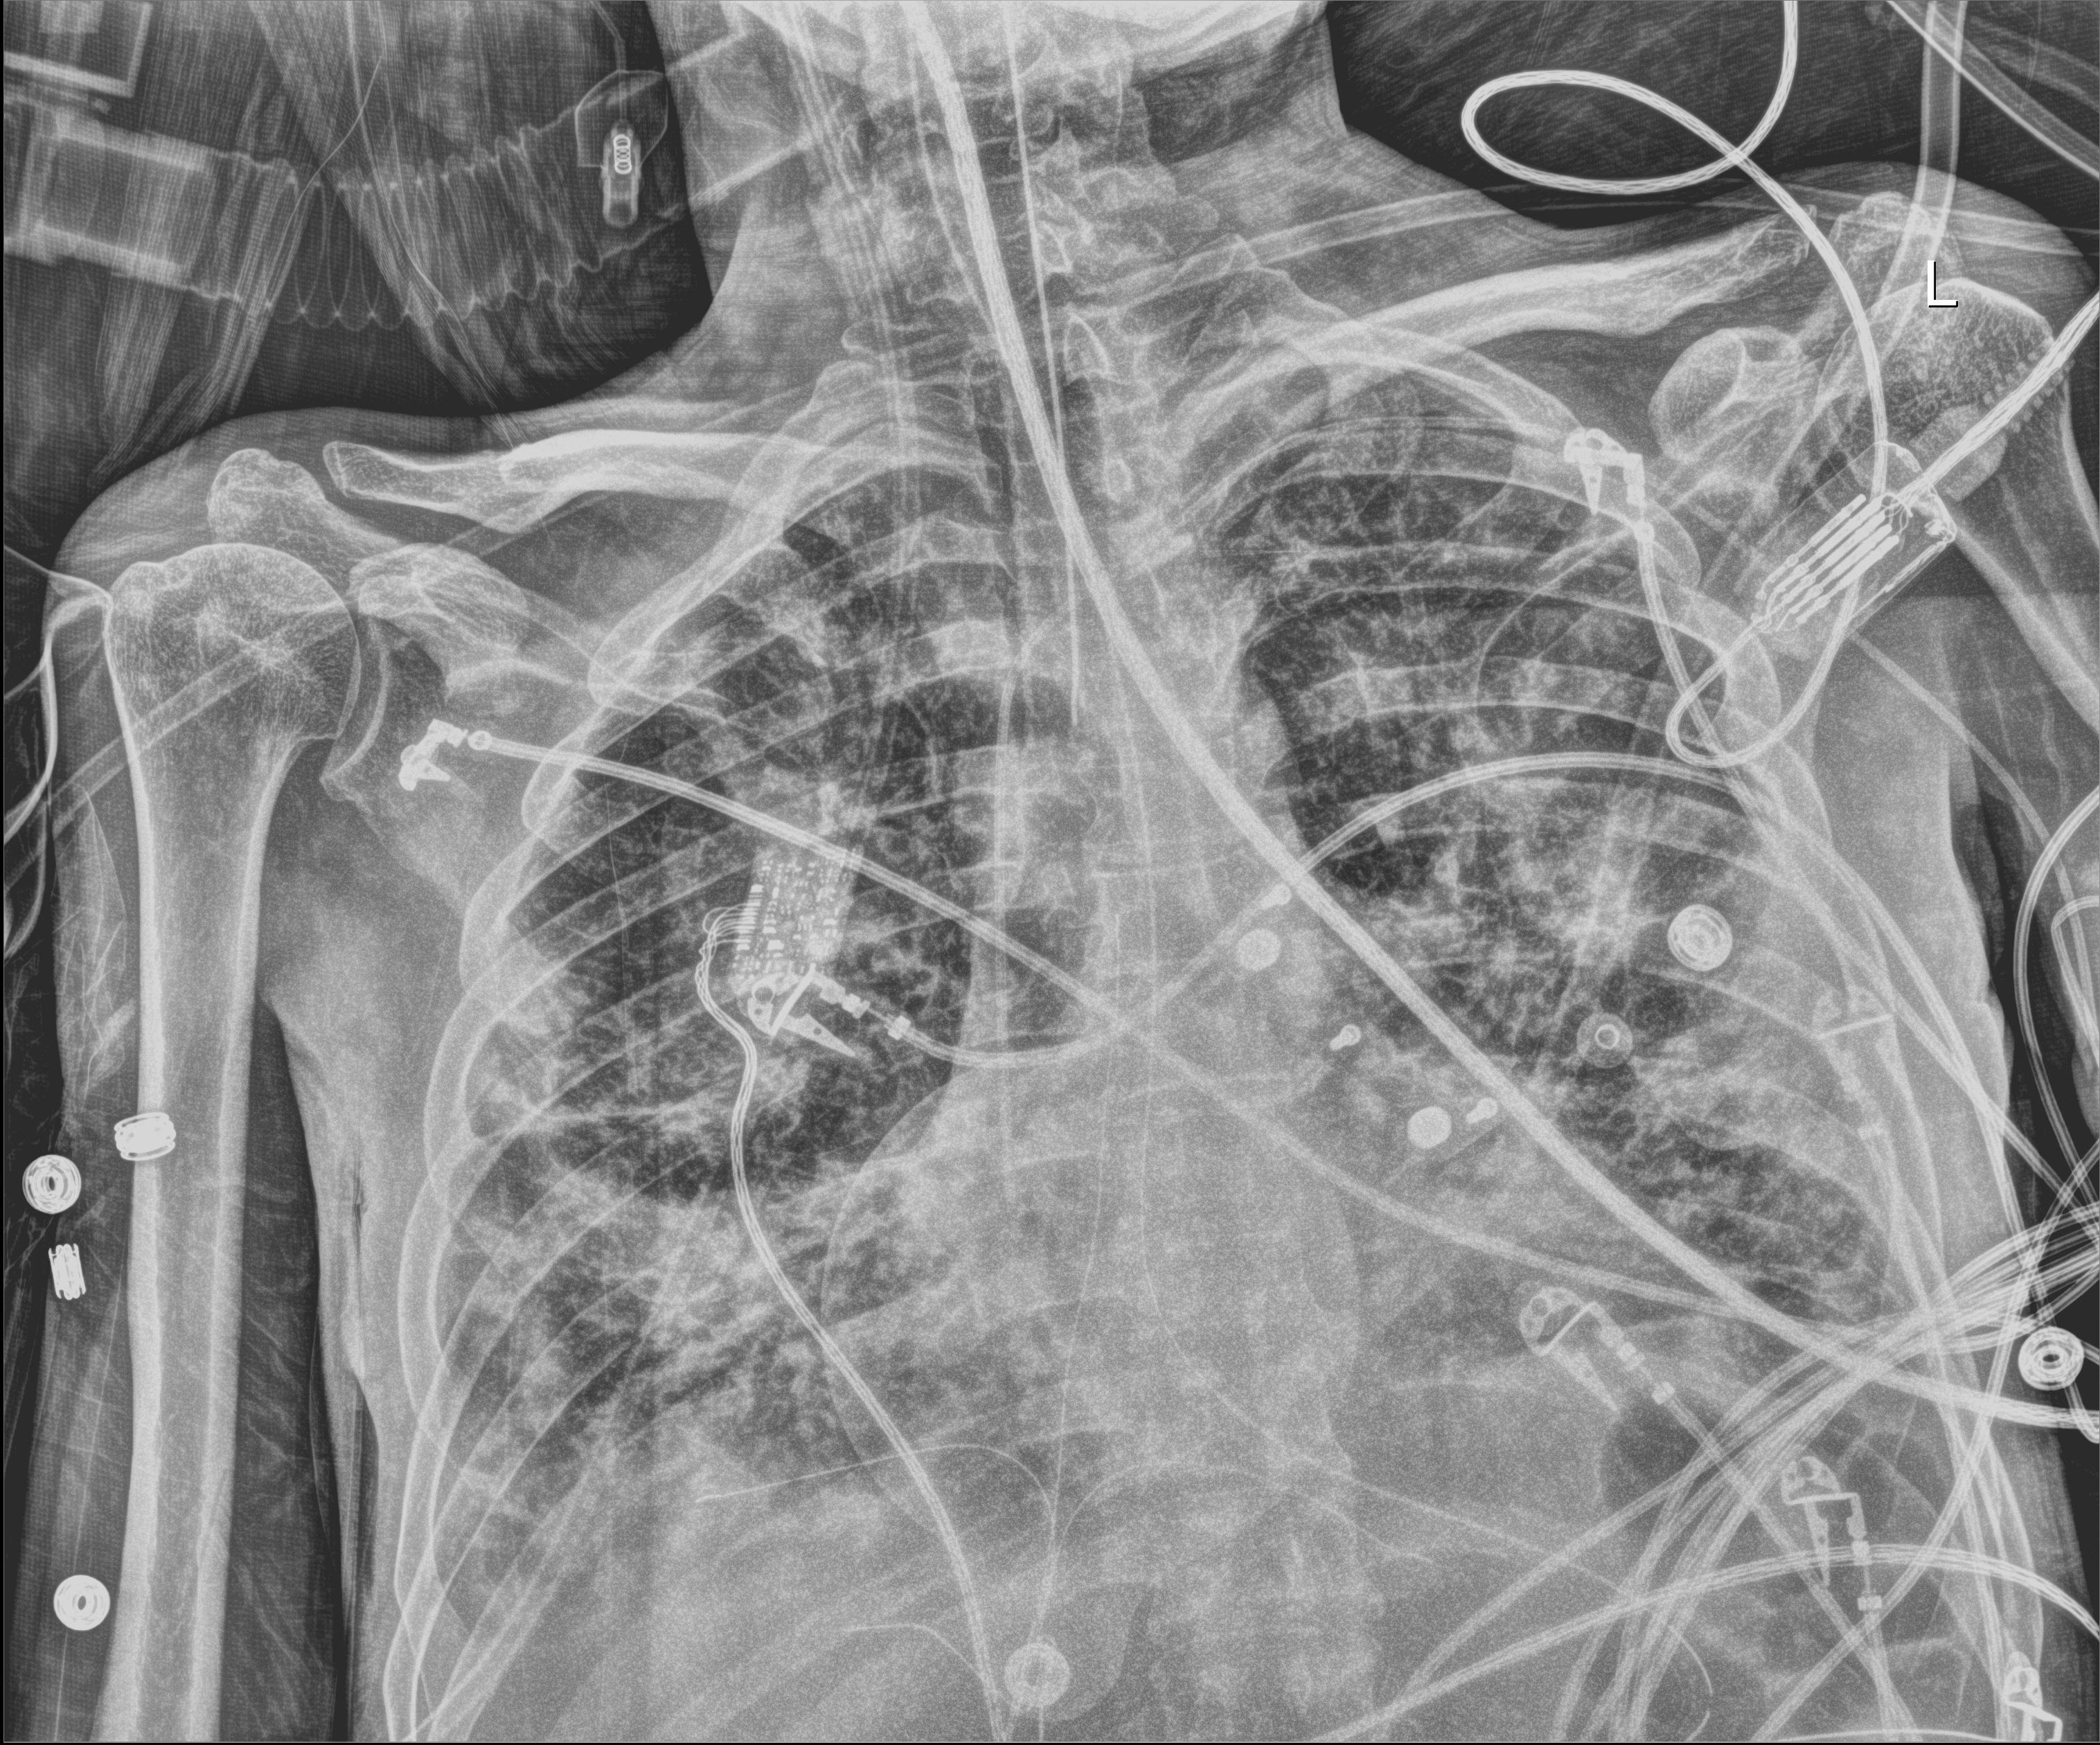
Portable chest radiograph, anteroposterior (AP) projection. Patient hospitalised with COVID-19; male, aged 18–59 years.
Admission-level facts for this patient (not findings on this image; timing relative to this image not recorded):
- length of hospital stay: 96 days
- admitted to intensive care during this hospital stay: yes